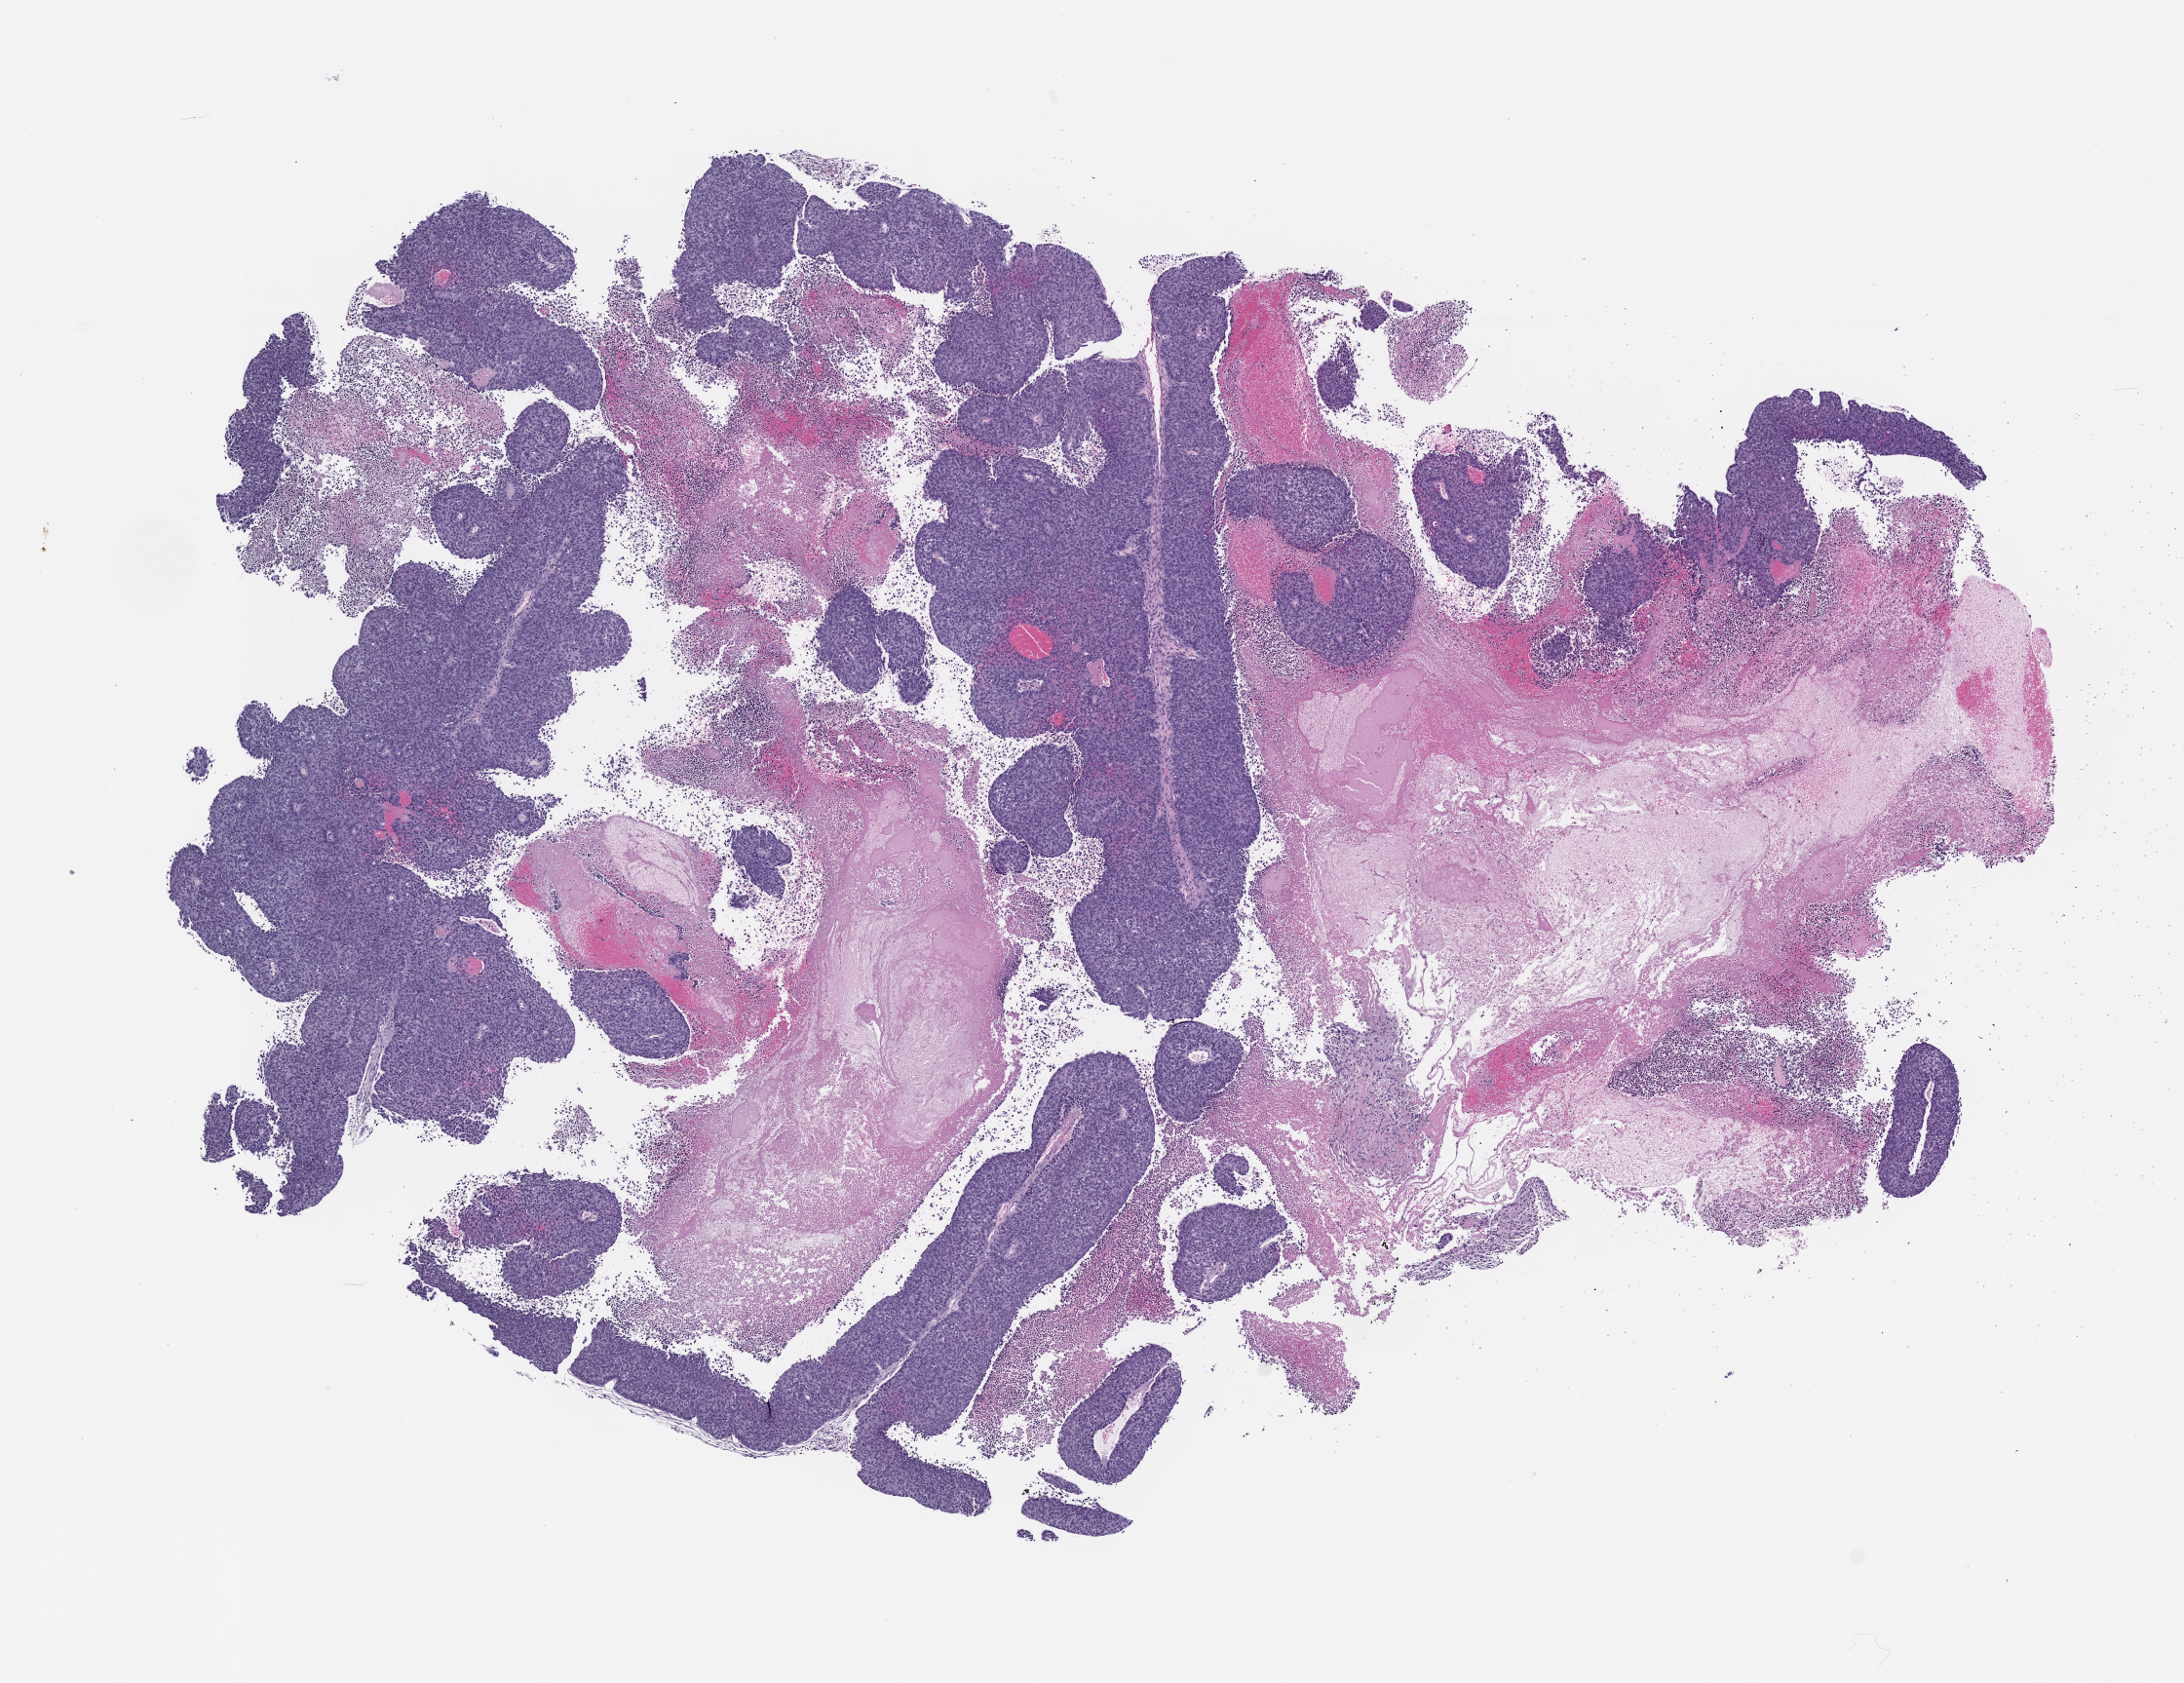
Whole-slide image, hematoxylin and eosin (H&E): patient-derived xenograft (human tumor grown in a mouse), passage 1, shown as a low-resolution overview of the whole scanned area (about 9.0 x 6.9 mm), formalin-fixed paraffin-embedded section, tumor site category: vagina.
Originating patient diagnosis: Vaginal Carcinoma.